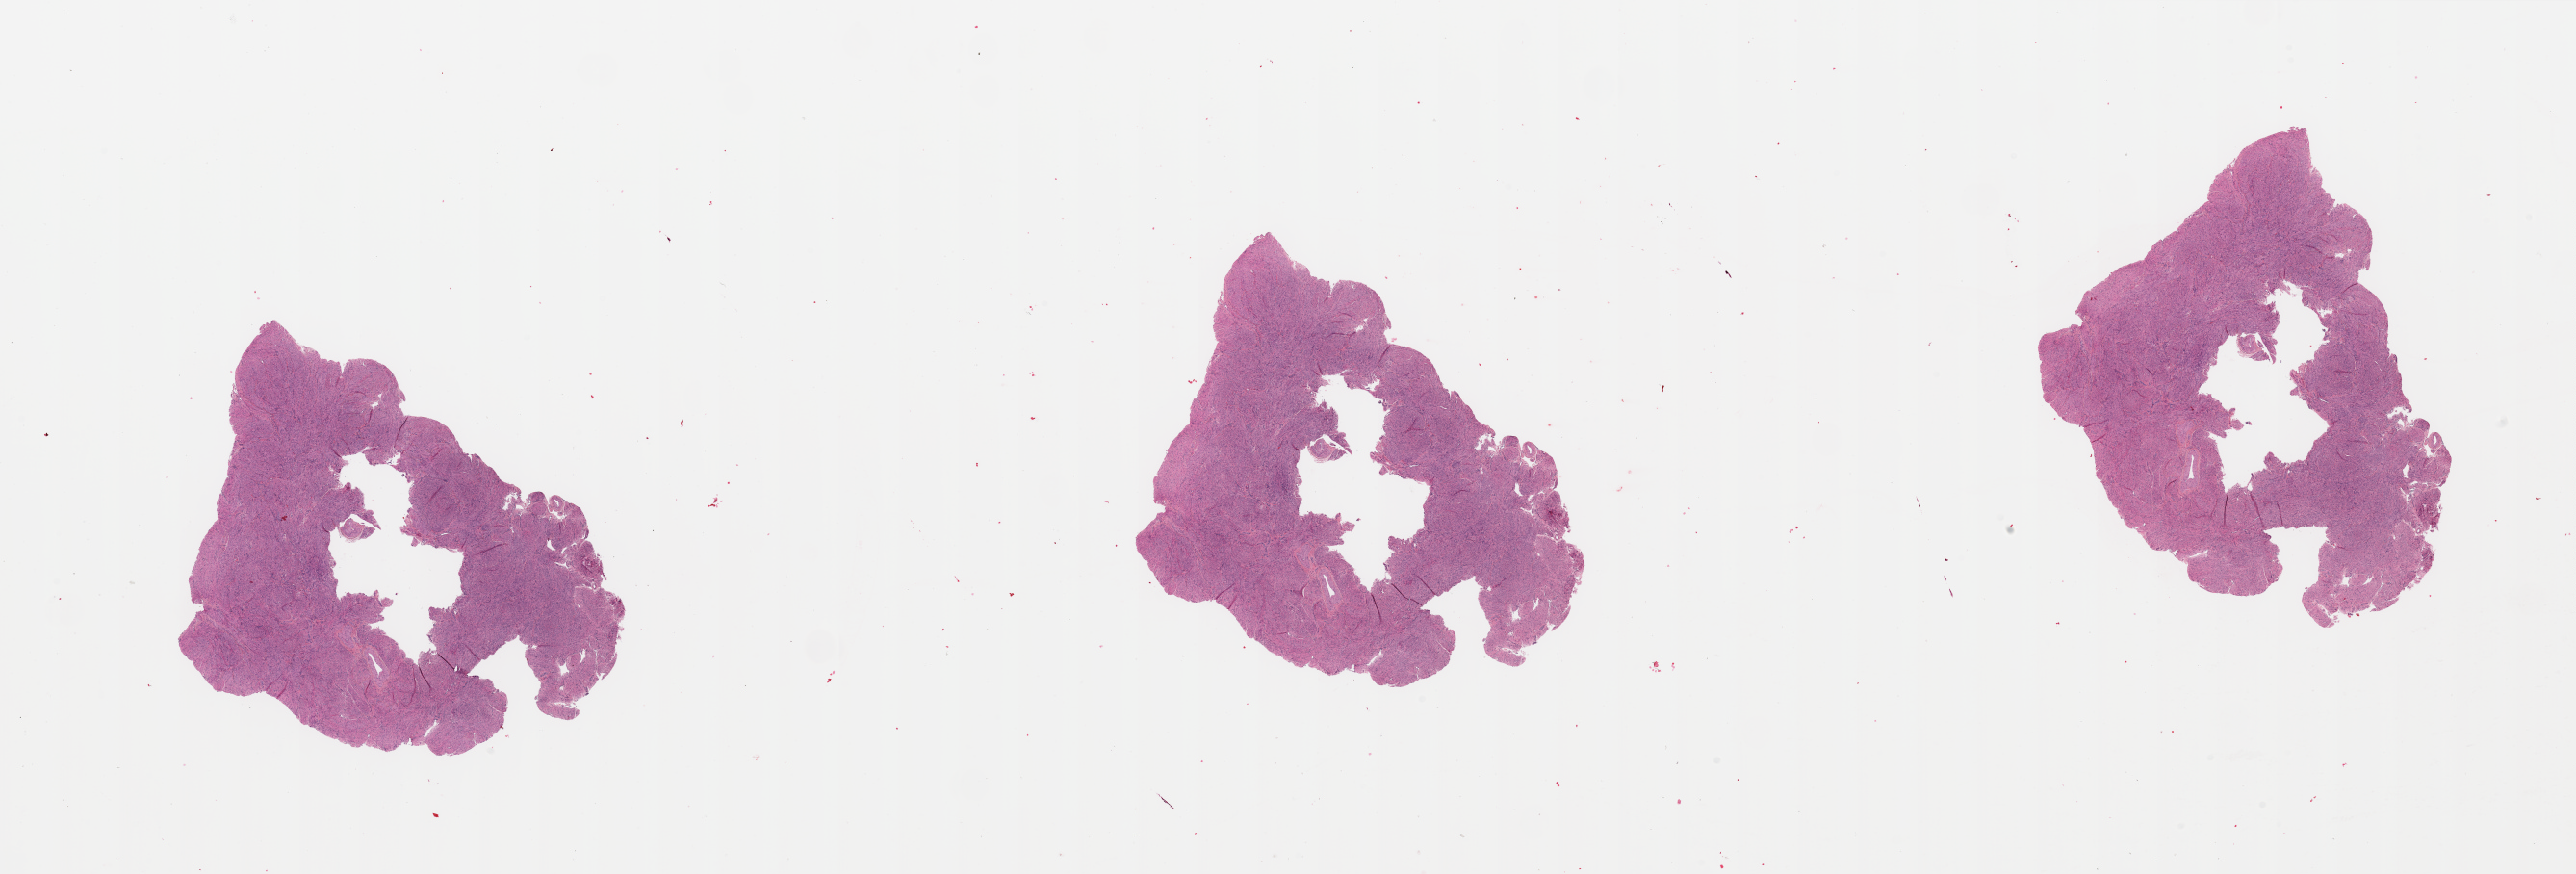
H&E whole-slide image, a low-resolution overview of the entire scanned area, about 42.3 x 14.4 mm (acquisition: 20x scan). Normal (non-tumour) tissue sample, sampled site: uterus. Female, 39 y/o.
- this section: normal (non-tumour) tissue from the same patient
- patient diagnosis: Endometrioid adenocarcinoma, NOS